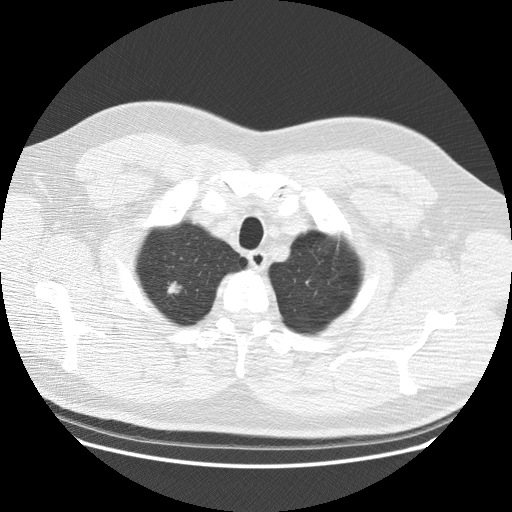
Low-dose screening chest CT, one axial slice; reconstruction kernel STANDARD; 120 kVp; lung window (W 1500 / L -600 HU); 2.5 mm slice thickness; 512 × 512 image matrix, field of view 389 × 389 mm.
Outlined on this slice (expert manual segmentation):
- lesion 1 (tumor, upper lobe of right lung): bounding box <167,281,182,294> (left, top, right, bottom; pixels)